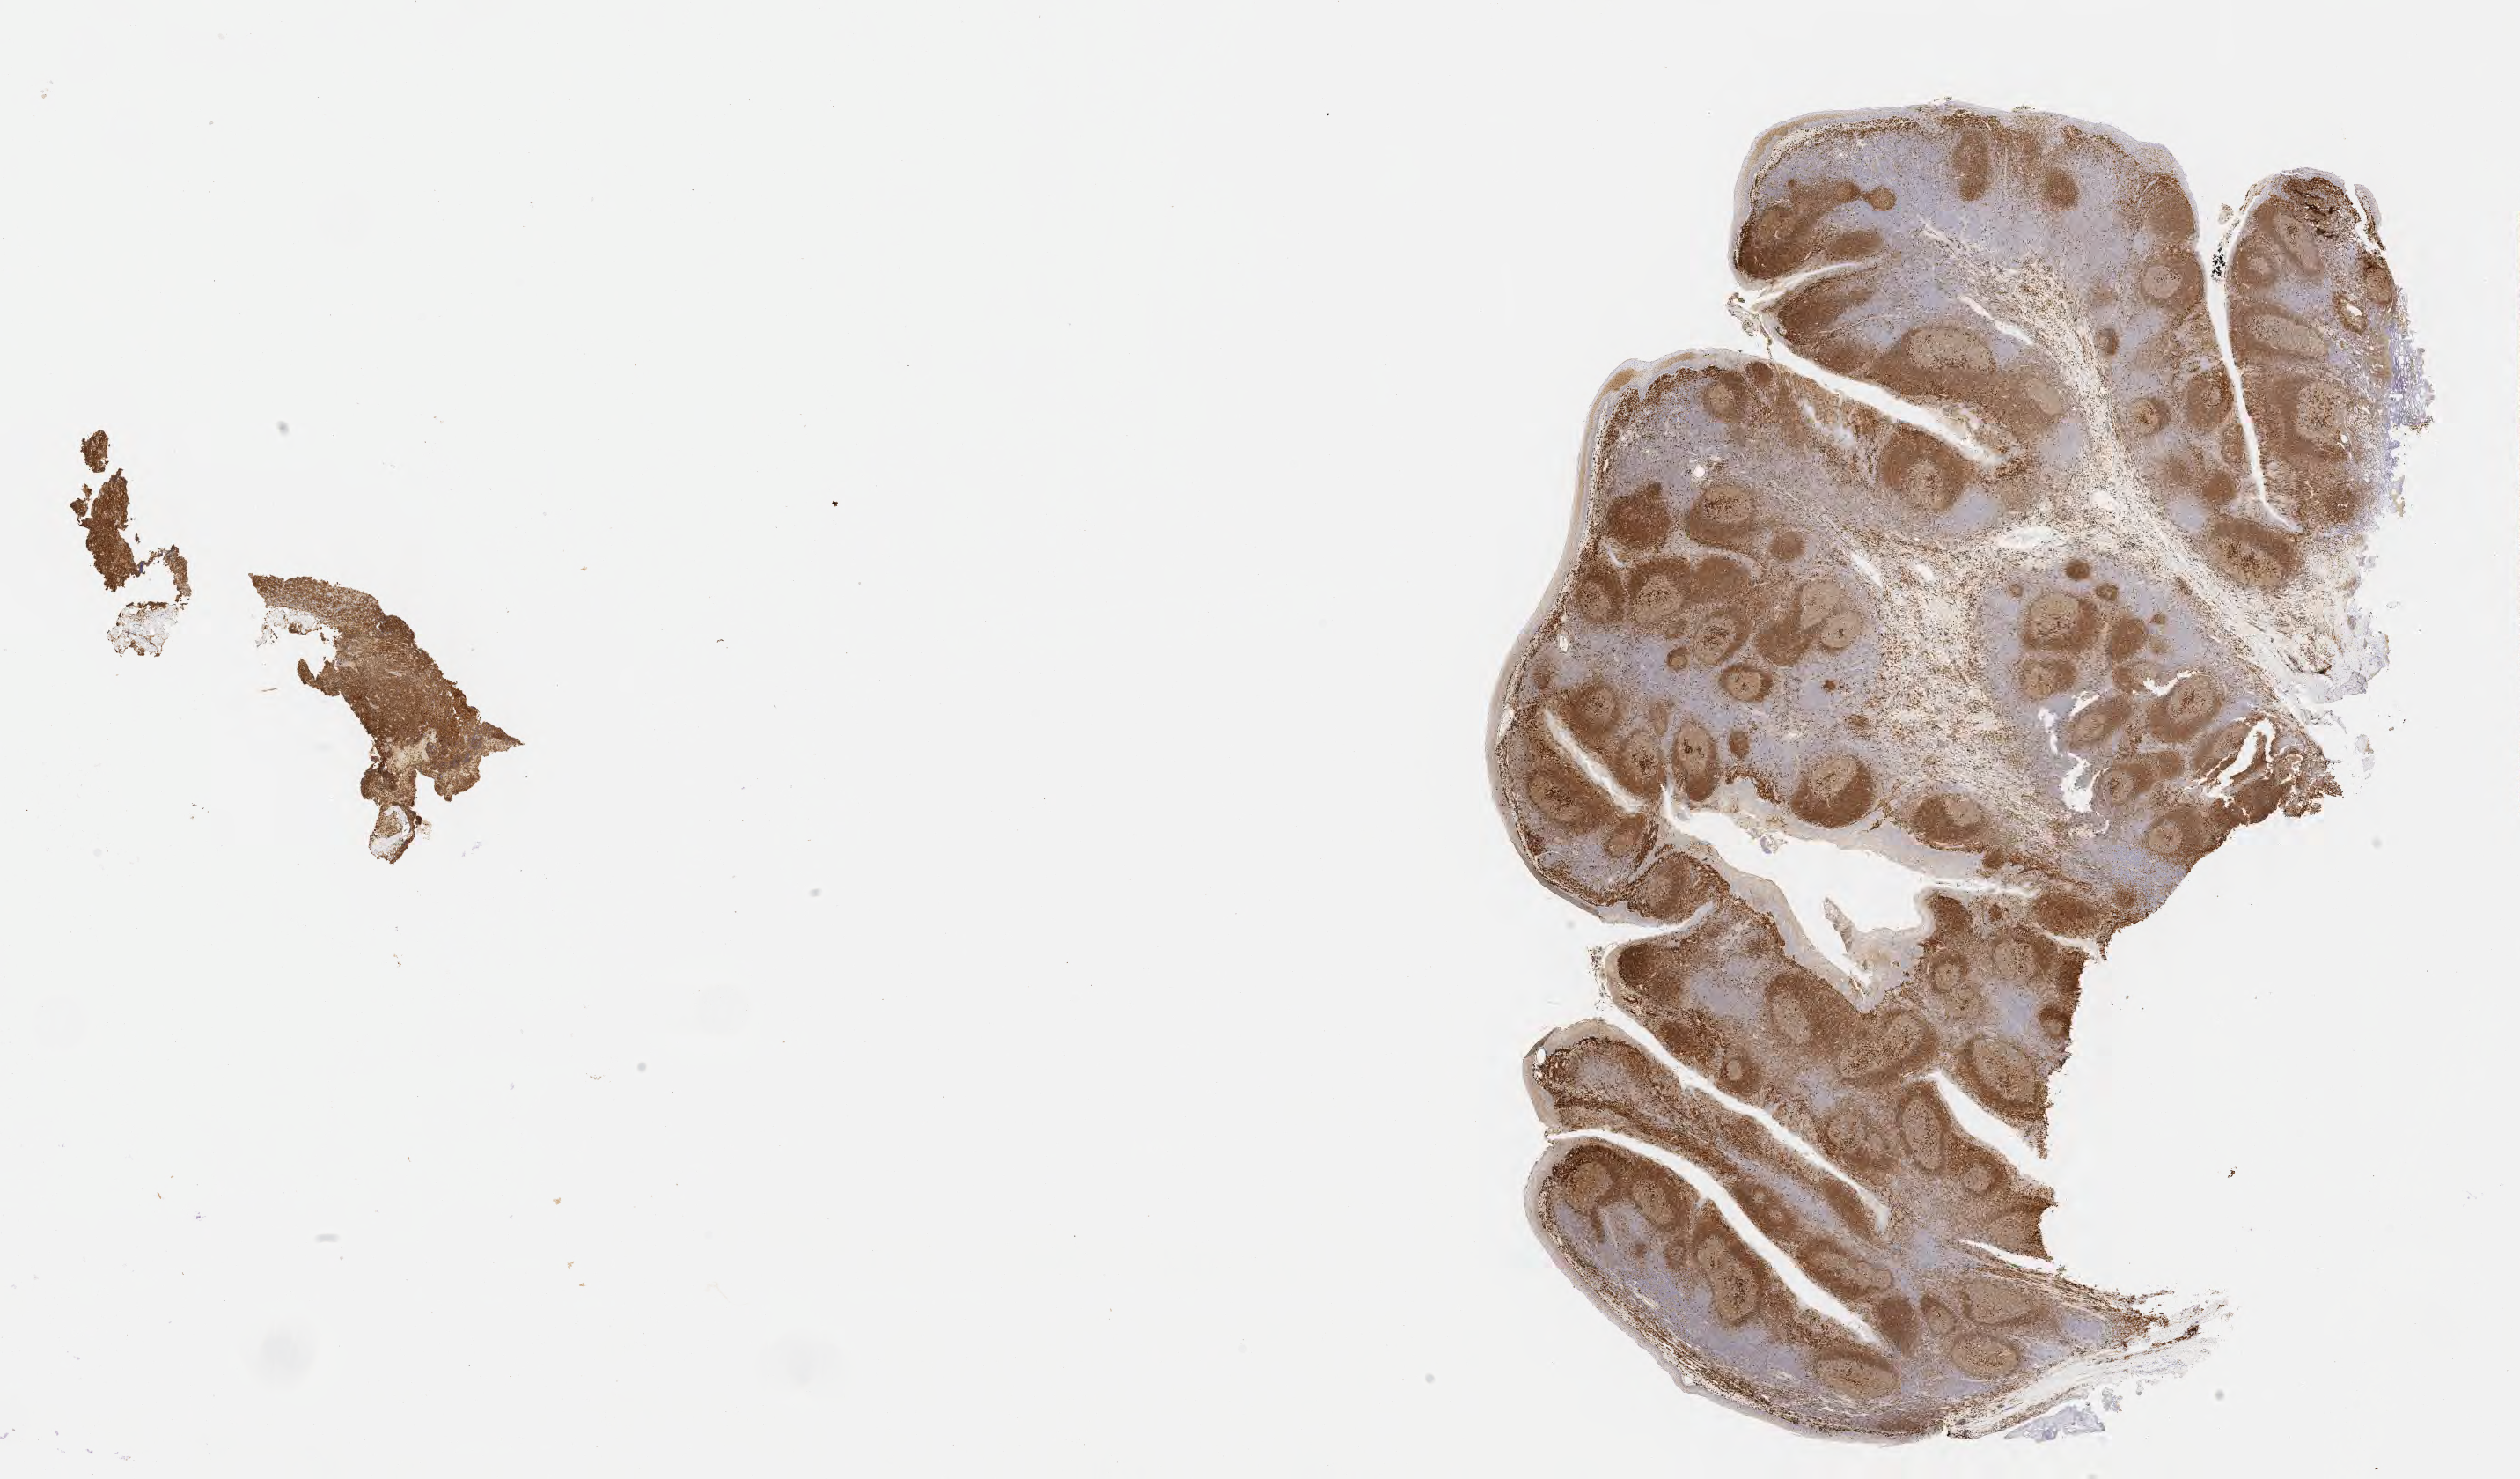
IHC for CD79a, whole-slide image, shown as a low-resolution overview of the whole scanned area (about 23.1 x 13.6 mm). Tumor tissue. Patient: female, aged 27.
Histologic diagnosis: Diffuse large B-cell lymphoma, NOS.